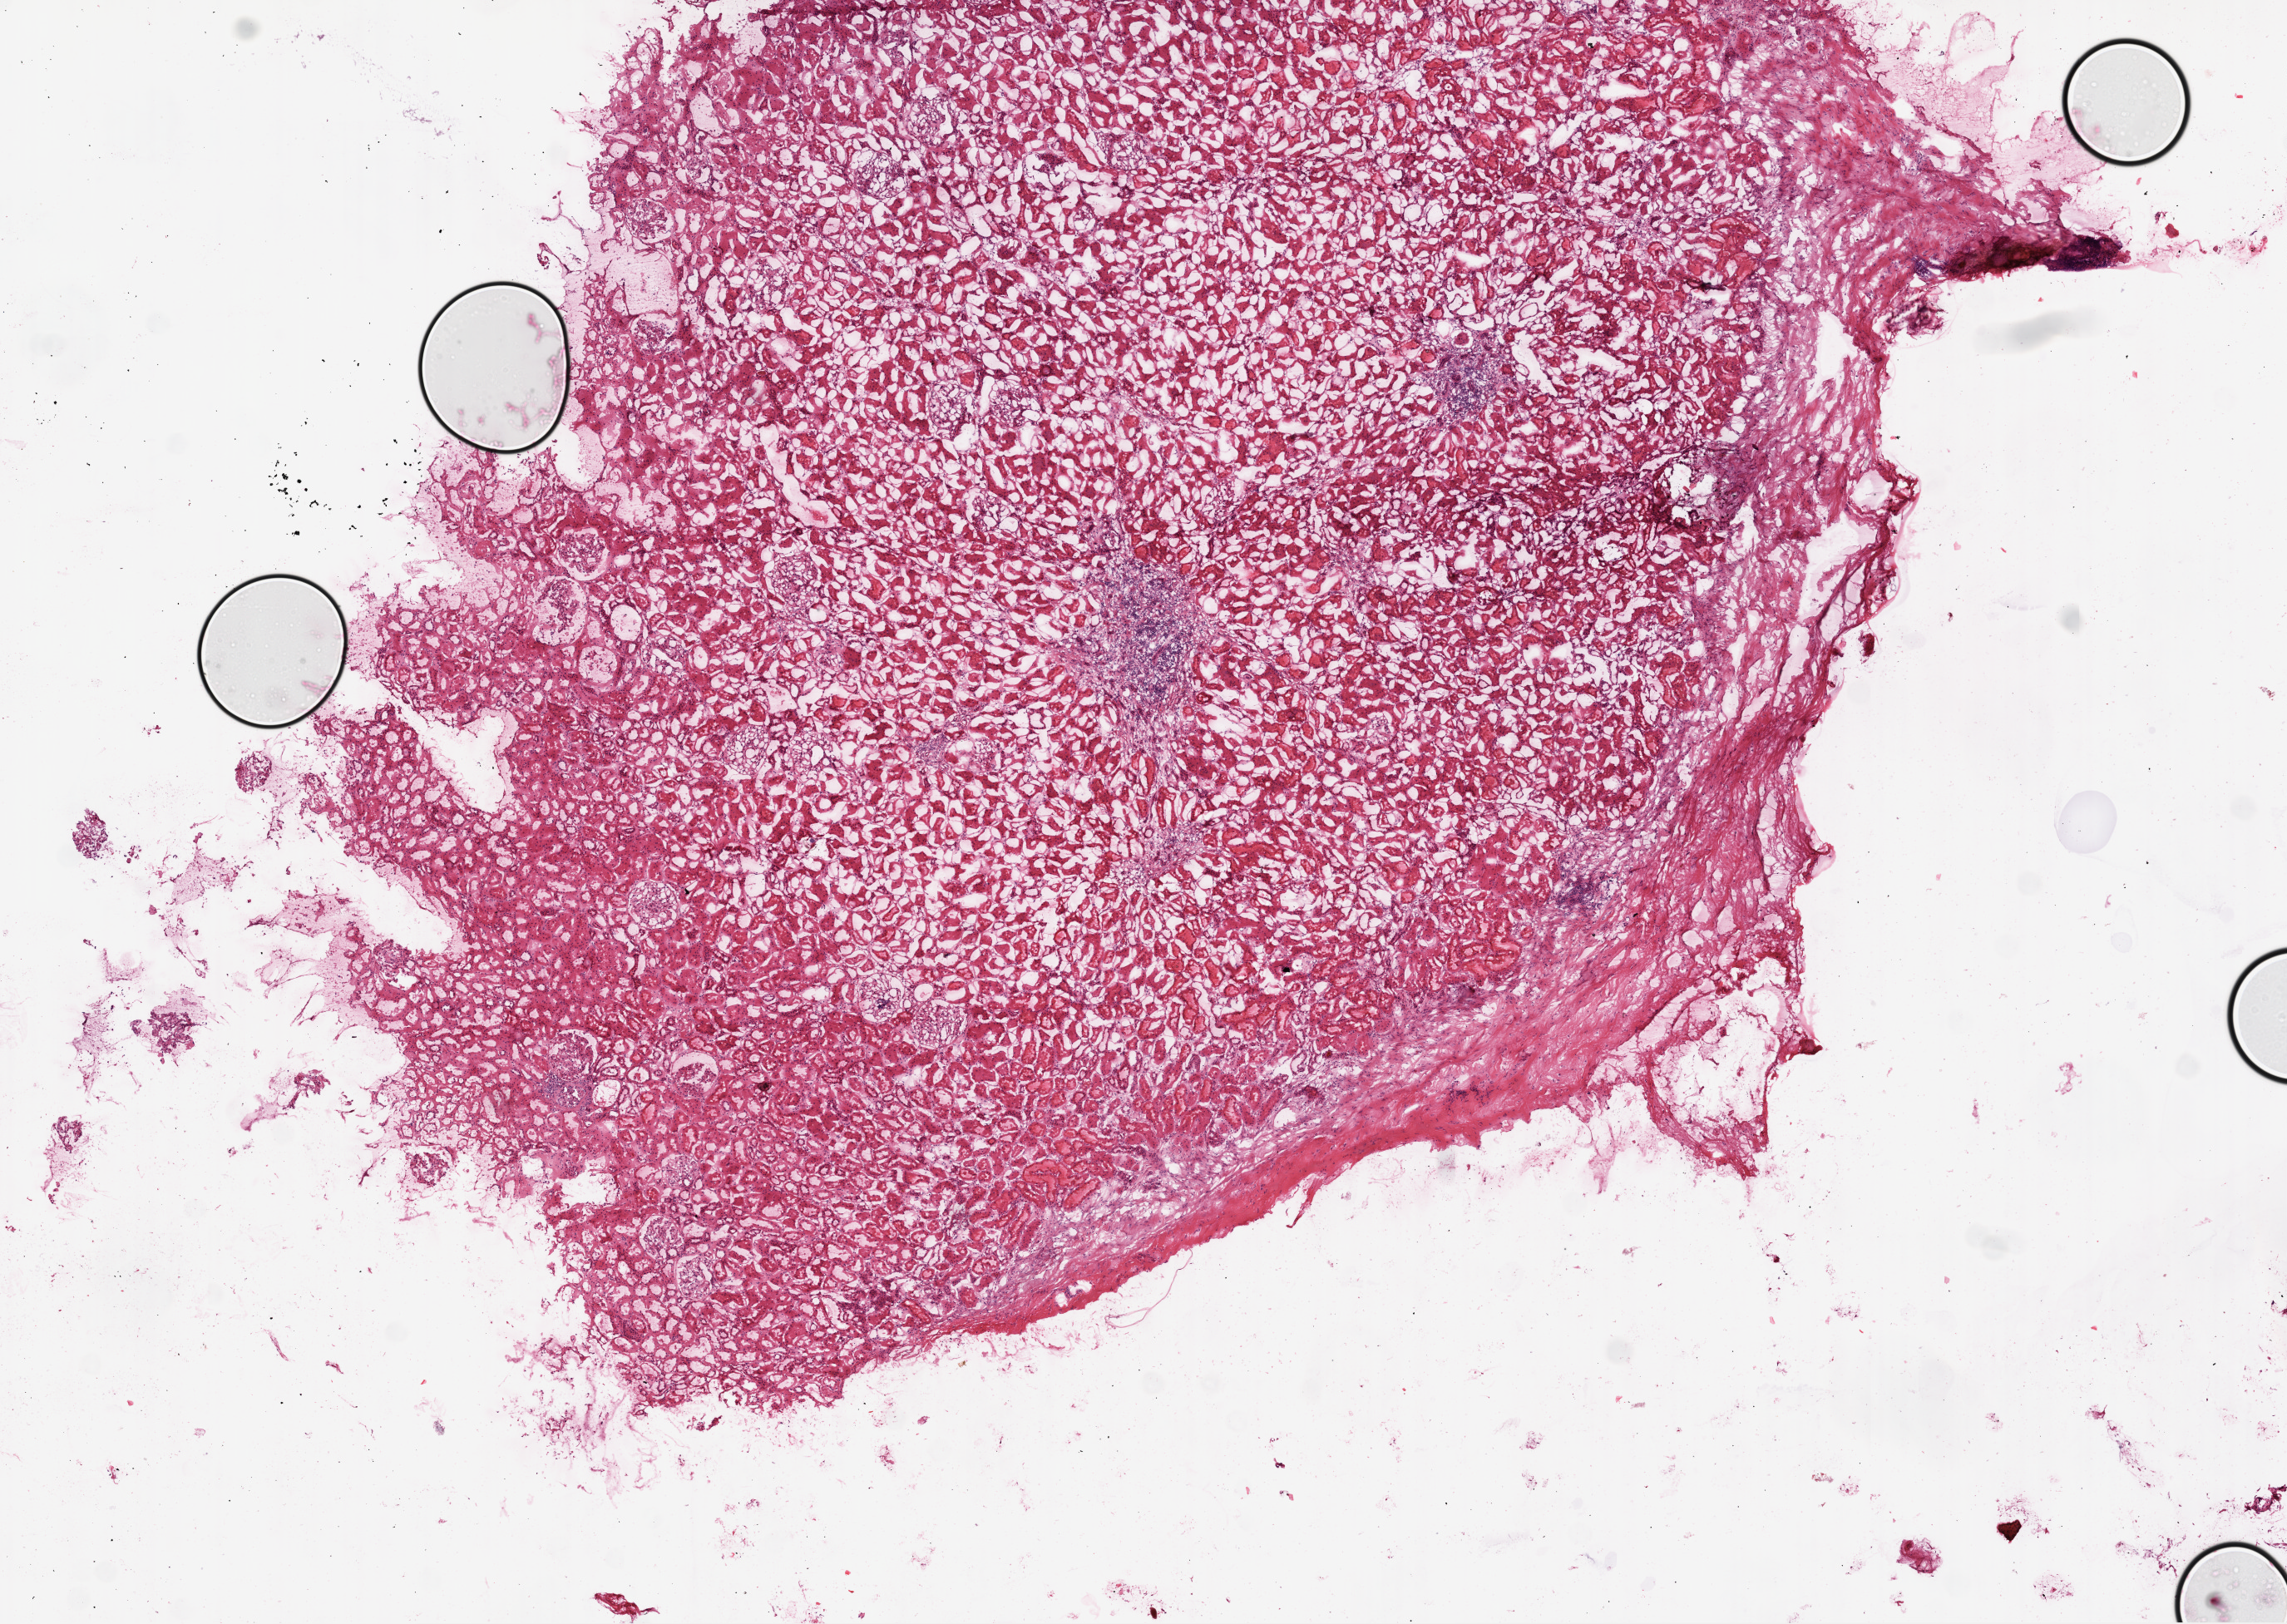
Digitized H&E tissue section (whole slide) — a low-resolution overview of the entire scanned area, about 11.0 x 7.8 mm, frozen section from the top of the tissue portion, kidney, solid tissue normal (non-tumour tissue) sample. Patient: male, age at initial diagnosis 40 years.
This section: solid tissue normal (non-tumour) sample from the same patient. Patient diagnosis: Clear cell adenocarcinoma, NOS.